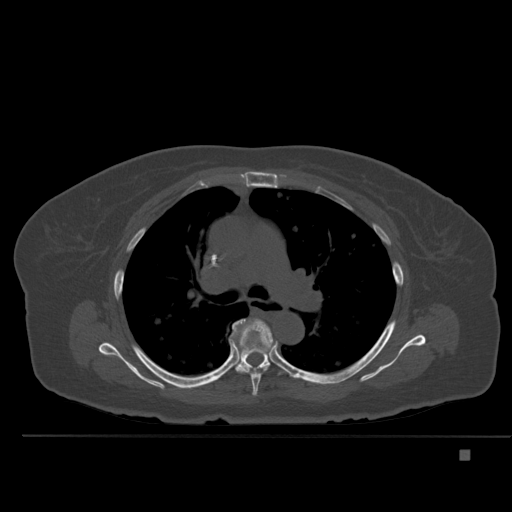
CT including the spine, one axial slice; slice 347 of 477 in the series (ordered by position); bone window (W 1800 / L 400 HU); 1.5 mm slice thickness; 512 × 512 image matrix. Patient: female, 74 years. Case-level facts recorded for this patient, not image findings: primary cancer: colon.
Structures marked on this image (semi-automatic segmentation, software-assisted and operator-edited):
- T5 vertebra: bounding box [x1, y1, x2, y2] px = [237, 319, 274, 396]
- T6 vertebra: [229, 319, 288, 375]